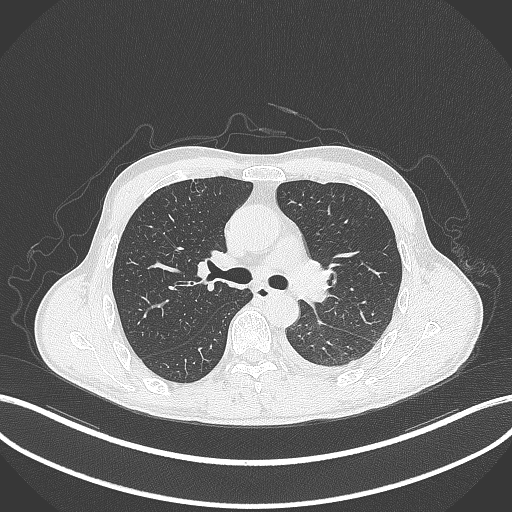
Chest CT, one axial slice; reconstruction kernel B70f; 120 kVp; lung window (W 1500 / L -600 HU); 1 mm slice thickness; 512 × 512 image matrix. Male patient, age 47 years. Case-level facts recorded for this patient, not image findings: clinical TNM (as recorded): T3 N1 M1c; histopathological grade: G3.
Structures marked on this image (bounding box drawn by a radiologist):
- lung tumour (recorded histology: small cell carcinoma): bounding box <305,285,330,303> (left, top, right, bottom; pixels)